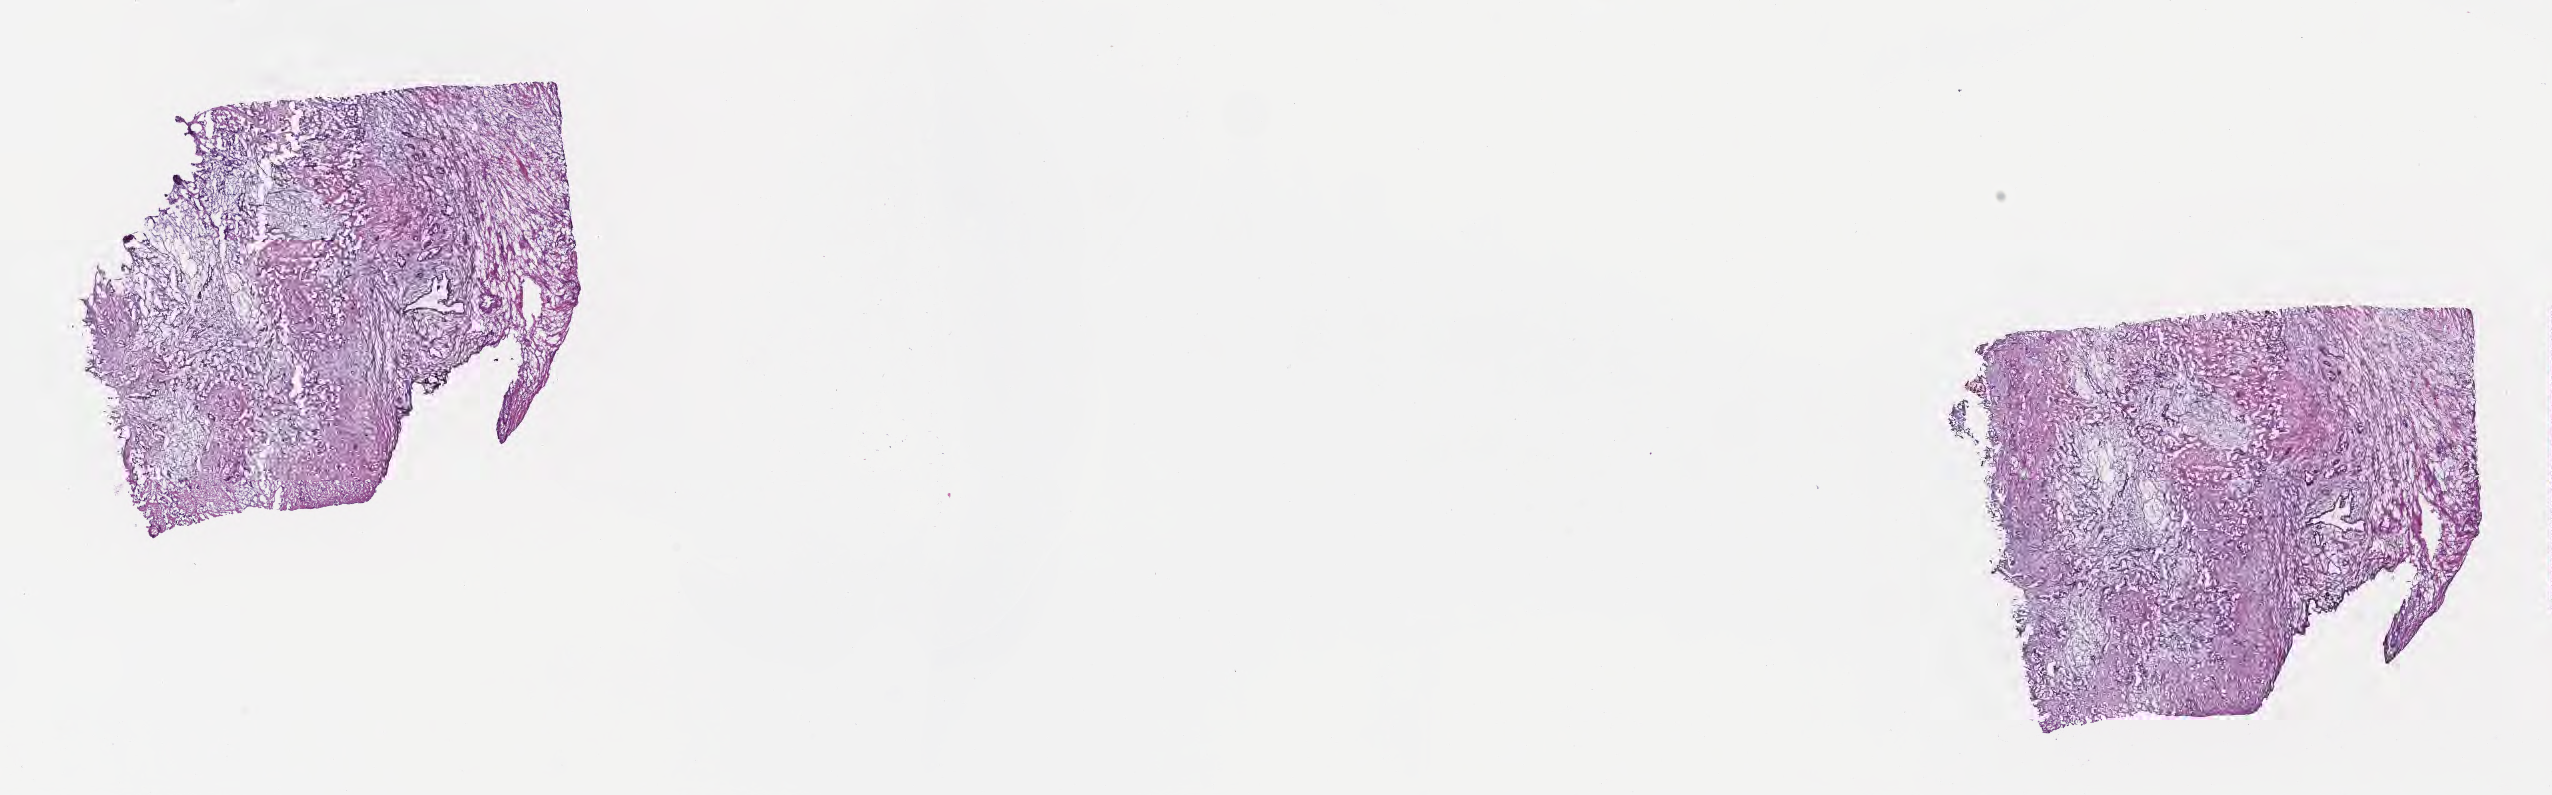
Haematoxylin and eosin whole-slide image — low-resolution overview of the scanned area, about 20.6 x 6.4 mm, cryosection, specimen: primary tumor, site: extrahepatic bile duct. Female, age 75 years at initial diagnosis. Pathologist review of this section (percent, as recorded): tumor cells 70%, tumor nuclei 70%, stromal cells 30%, necrosis 0%, normal cells 0%. Infiltration values recorded for this section: lymphocyte infiltration 6%, monocyte infiltration 3%, neutrophil infiltration 9%.
AJCC pathologic stage: Stage IIIB. Section: top of the tissue portion. Diagnosis: Cholangiocarcinoma.